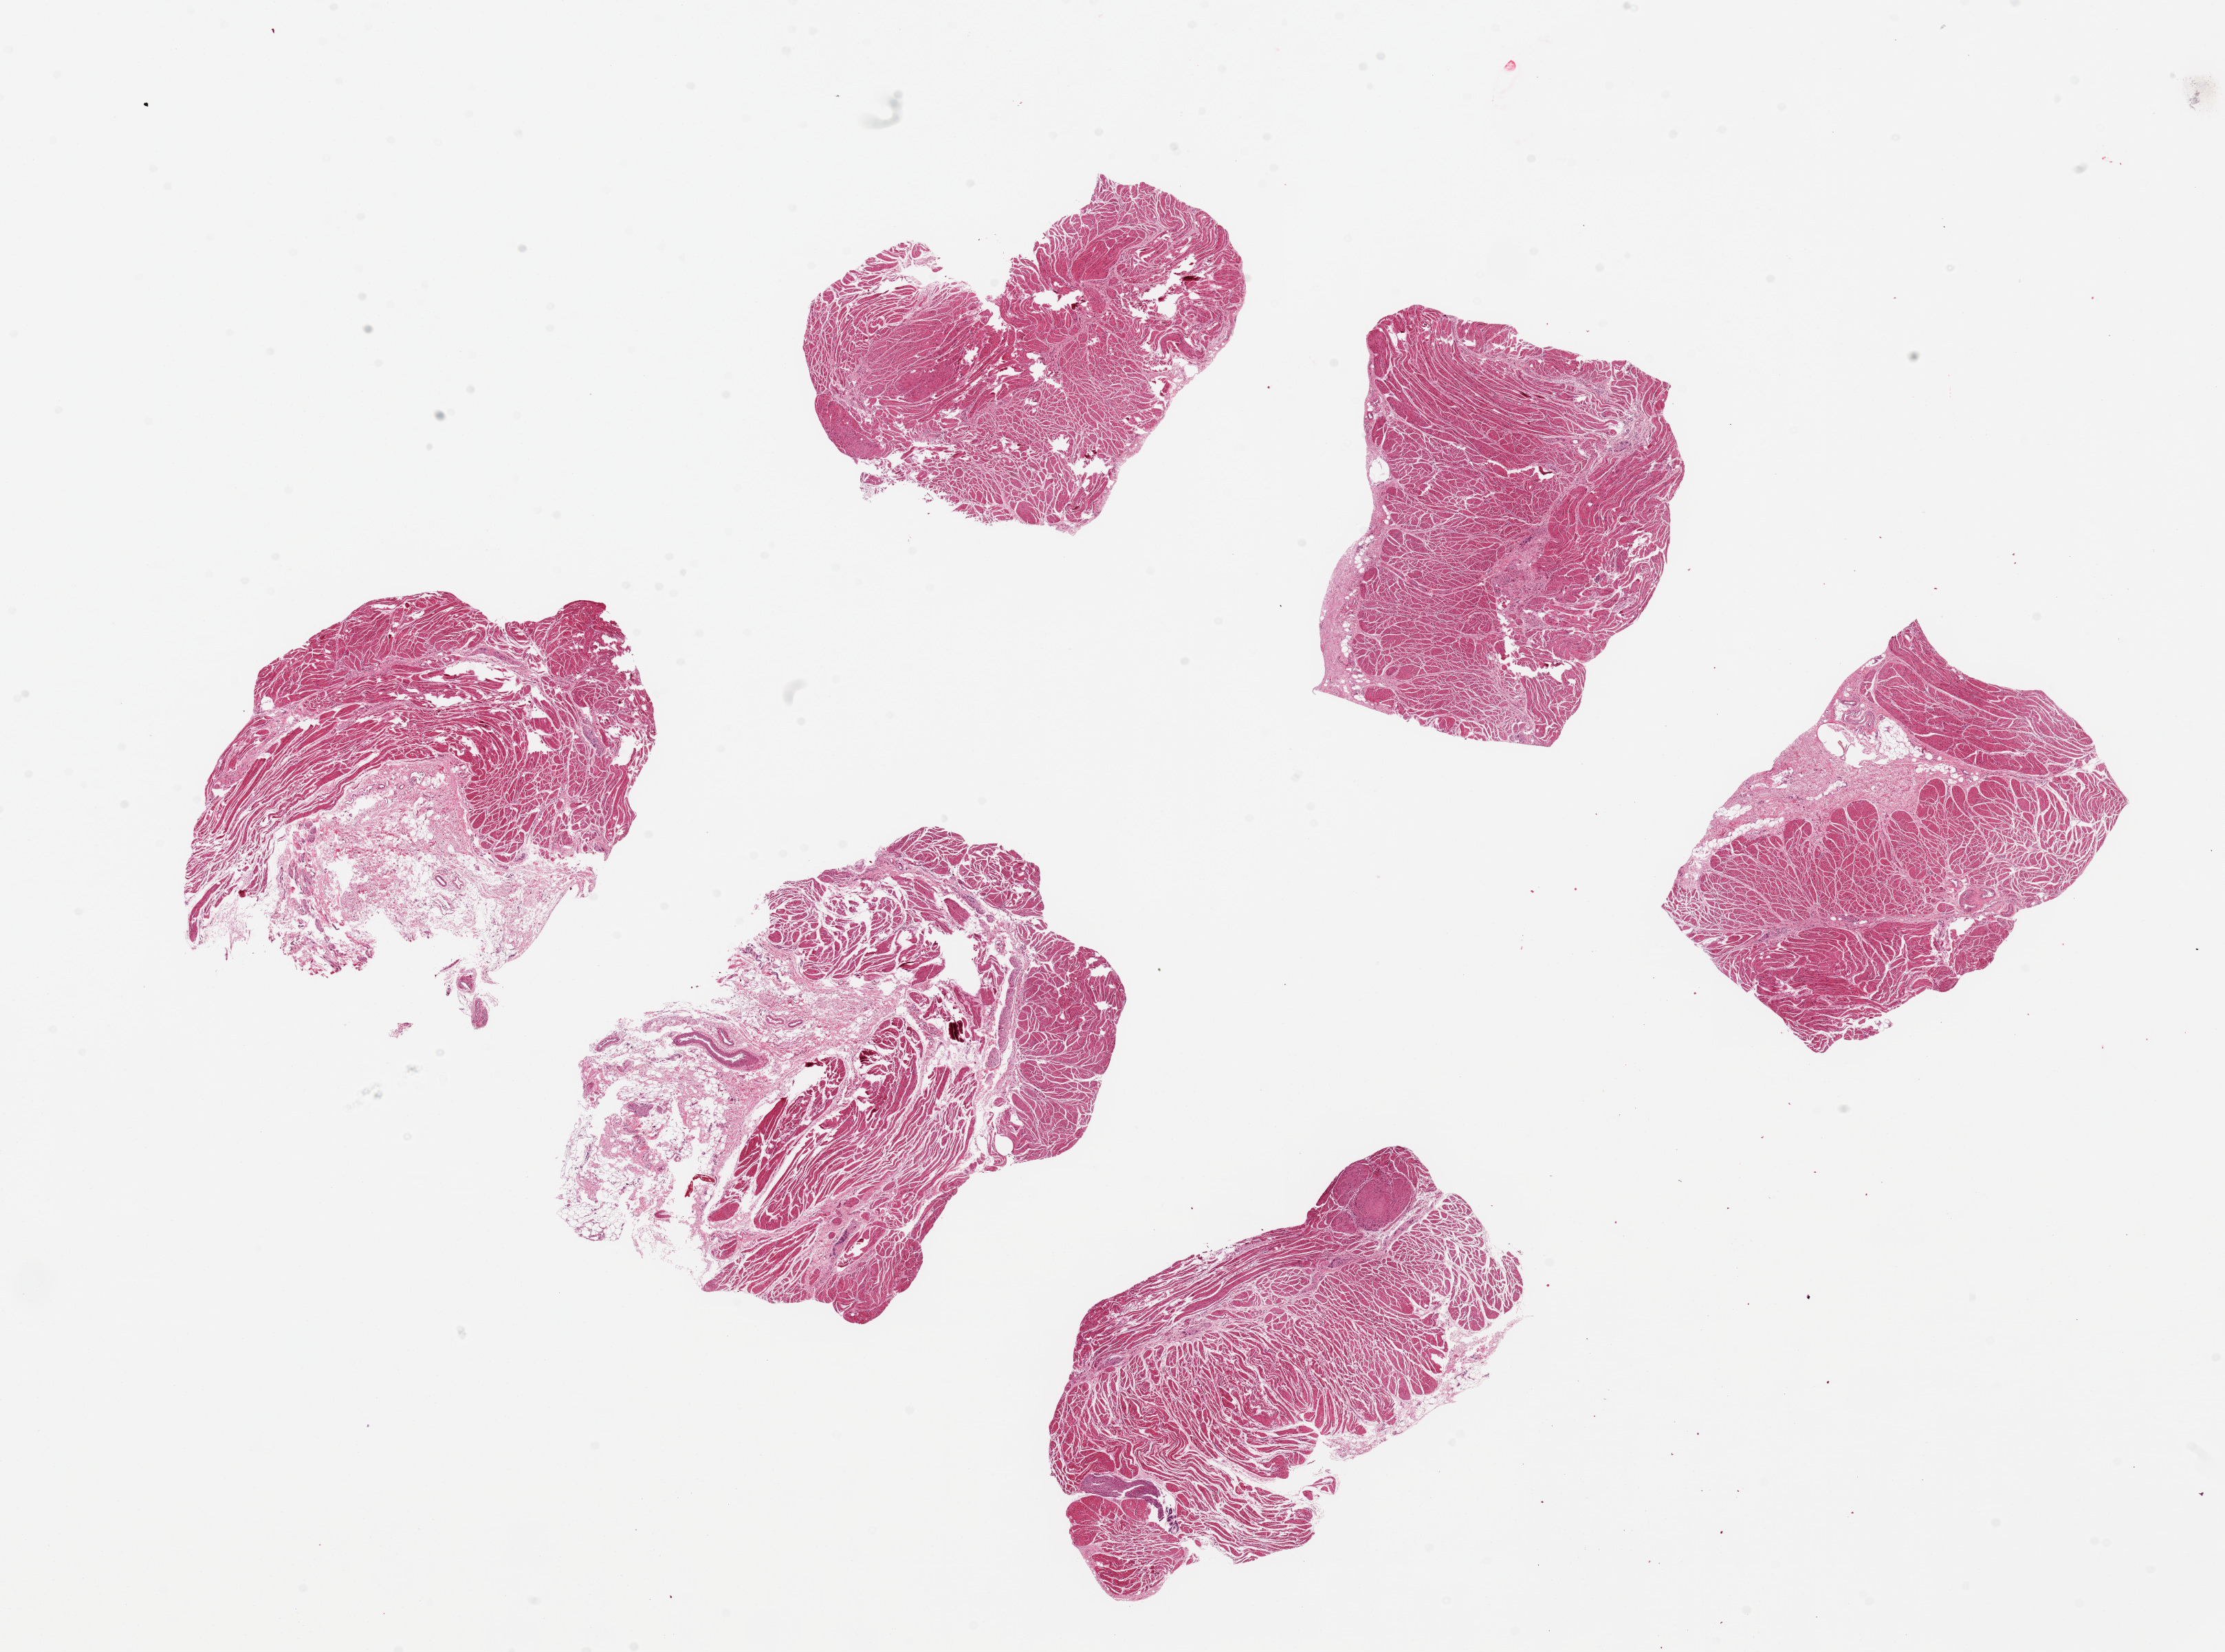
Whole-slide image, hematoxylin and eosin (H&E) stain, brightfield, a low-resolution overview of the entire scanned area, about 25.6 x 19.0 mm (acquisition: 20x scan); PAXgene-fixed, paraffin-embedded tissue; sampled site (target tissue): esophageal muscle; donor tissue sample. Donor: male.
- review note (as recorded): 6 ~5x4mm pieces